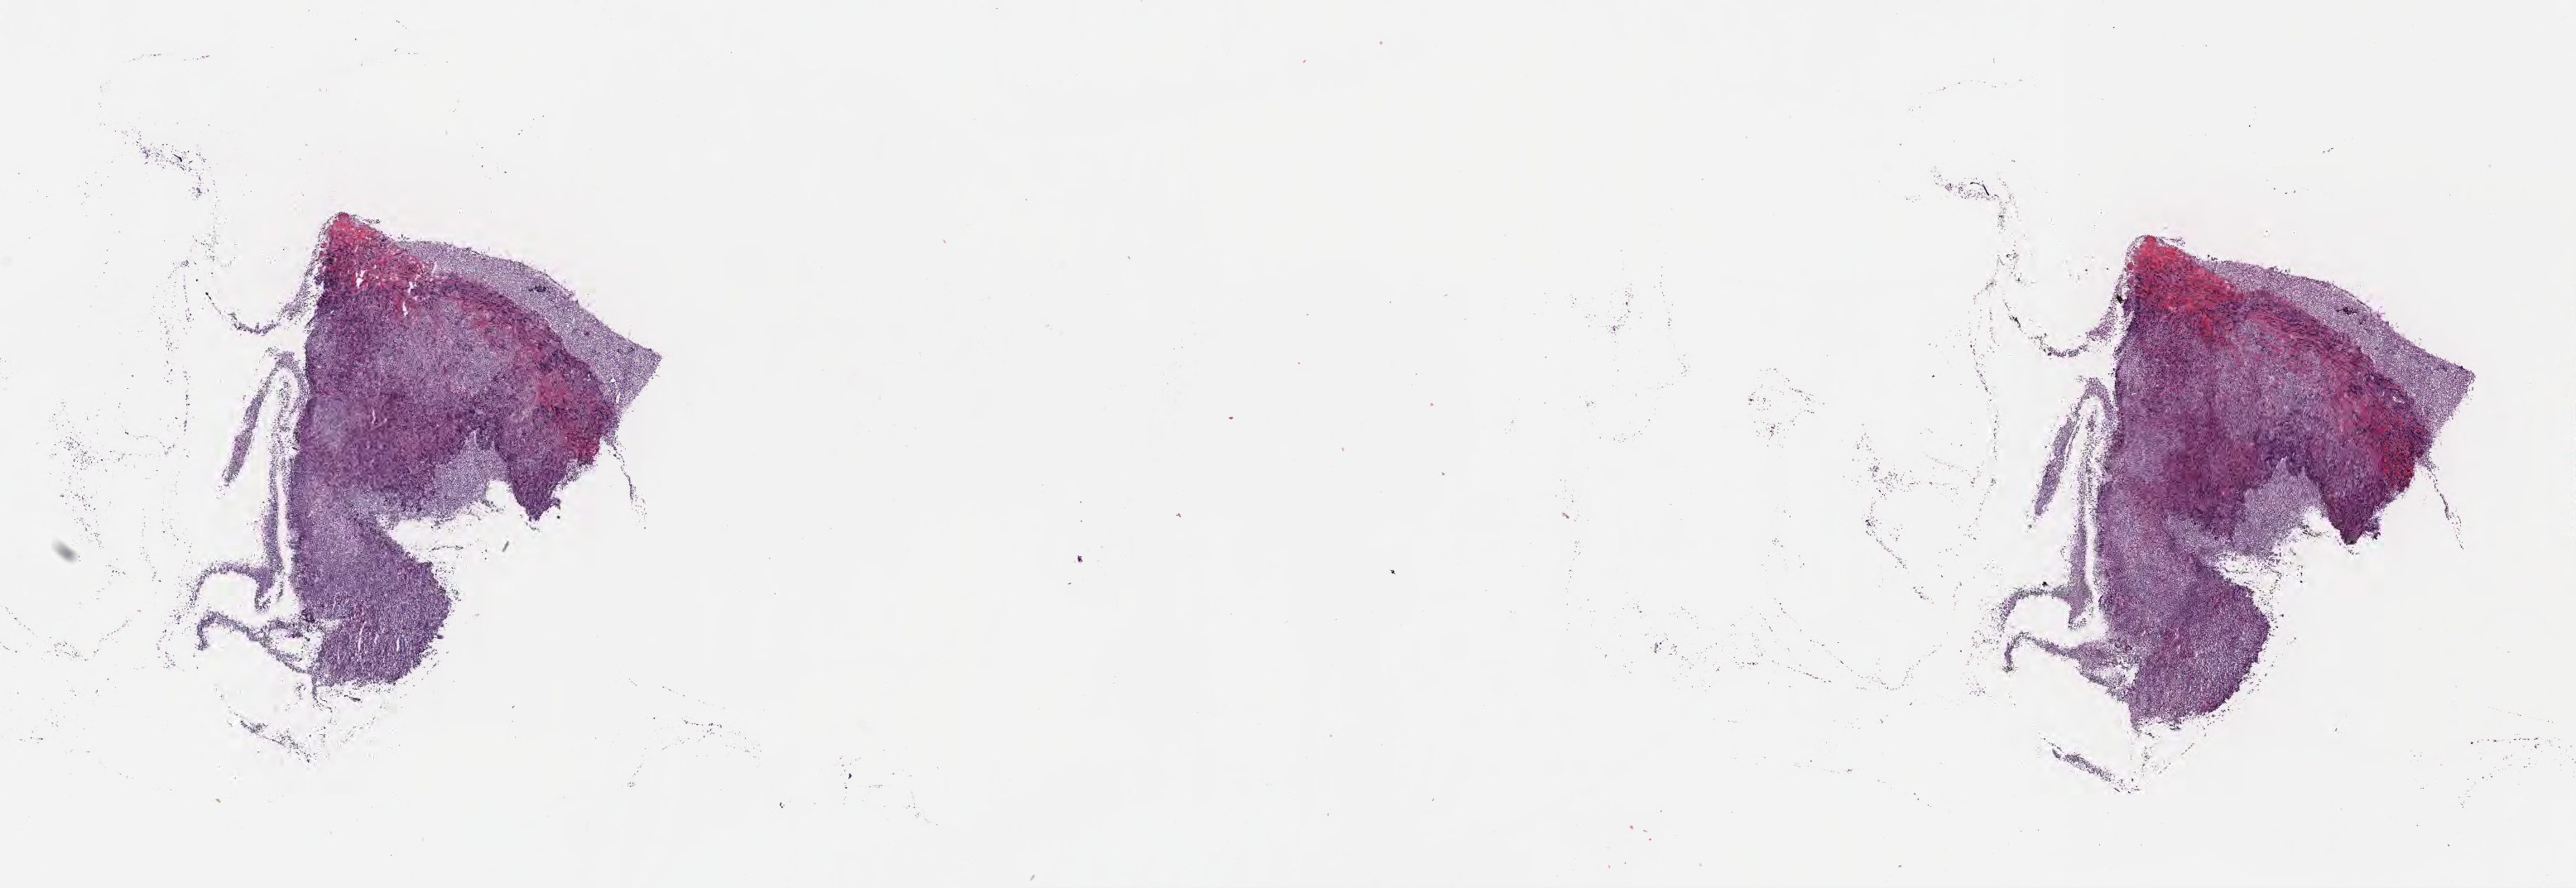
Whole-slide image, H&E stain — a low-resolution overview of the entire scanned area, about 25.1 x 8.7 mm. Cryosection. Specimen: primary tumor. Site: cranium. Patient male; 12 years old. Slide review estimates, as recorded: tumor cells 90%, tumor nuclei 95%, stromal cells 5%, necrosis 5%, normal cells 0%. Inflammatory infiltration, as recorded: lymphocyte infiltration 80%, monocyte infiltration 10%, neutrophil infiltration 0%.
* histologic diagnosis: Diffuse large B-cell lymphoma, NOS
* section: top of the tissue portion
* Ann Arbor stage (patient): Stage III